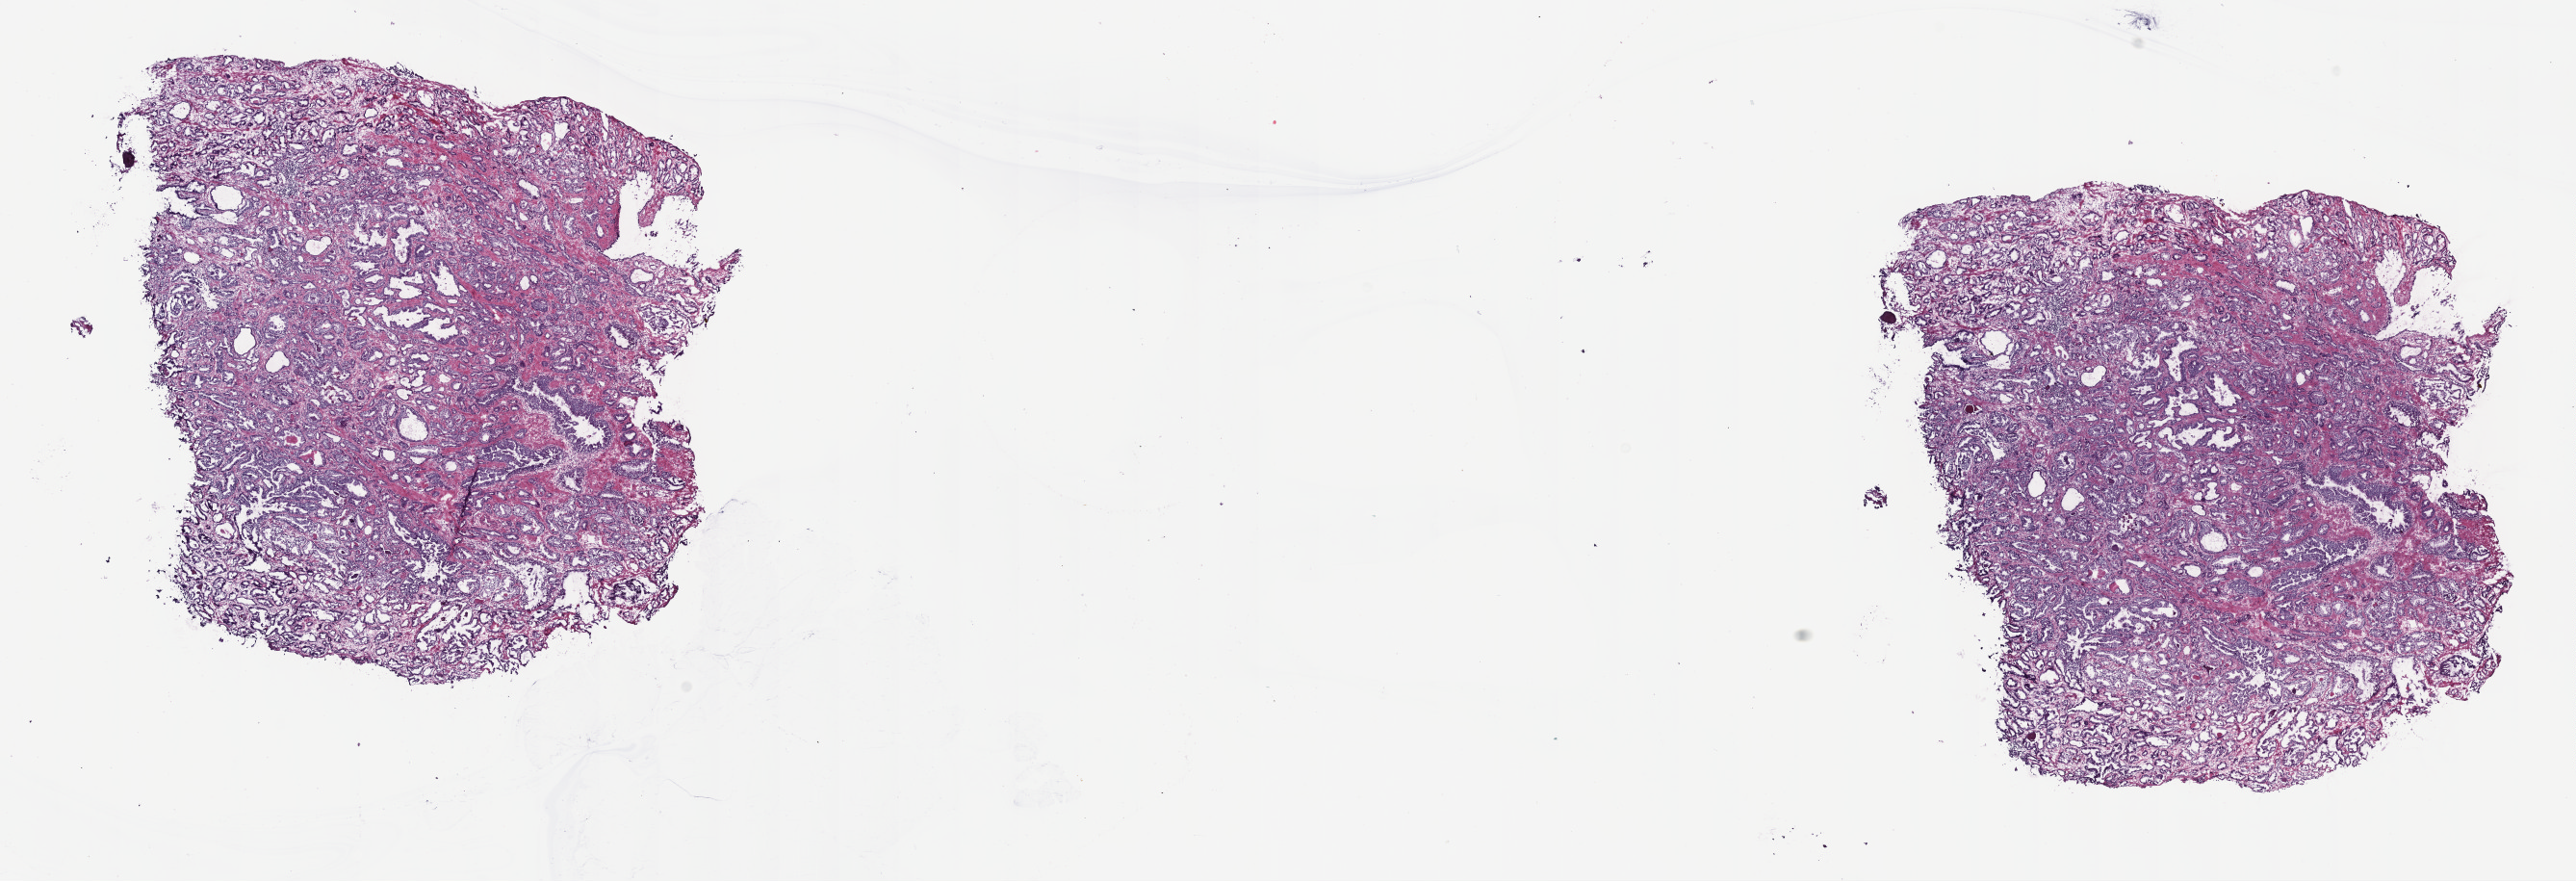
Digitized Hematoxylin and eosin (H&E) stained tissue section (whole slide), whole scanned area (about 21.6 x 7.4 mm, acquisition: 40x scan) shown as a low-resolution overview. Frozen section. Sample: primary tumour, prostate. Male patient; age at initial diagnosis 57 years. Gleason score: 7 (3+4). Slide review estimates, as recorded: tumour cells 85%, tumour nuclei 90%, normal cells 0%, stromal cells 15%, necrosis 0%. Infiltration values recorded for this section: lymphocyte infiltration 0%, monocyte infiltration 0%, neutrophil infiltration 0%.
Pathologic diagnosis: Adenocarcinoma, NOS (prostate gland). Laterality: bilateral.